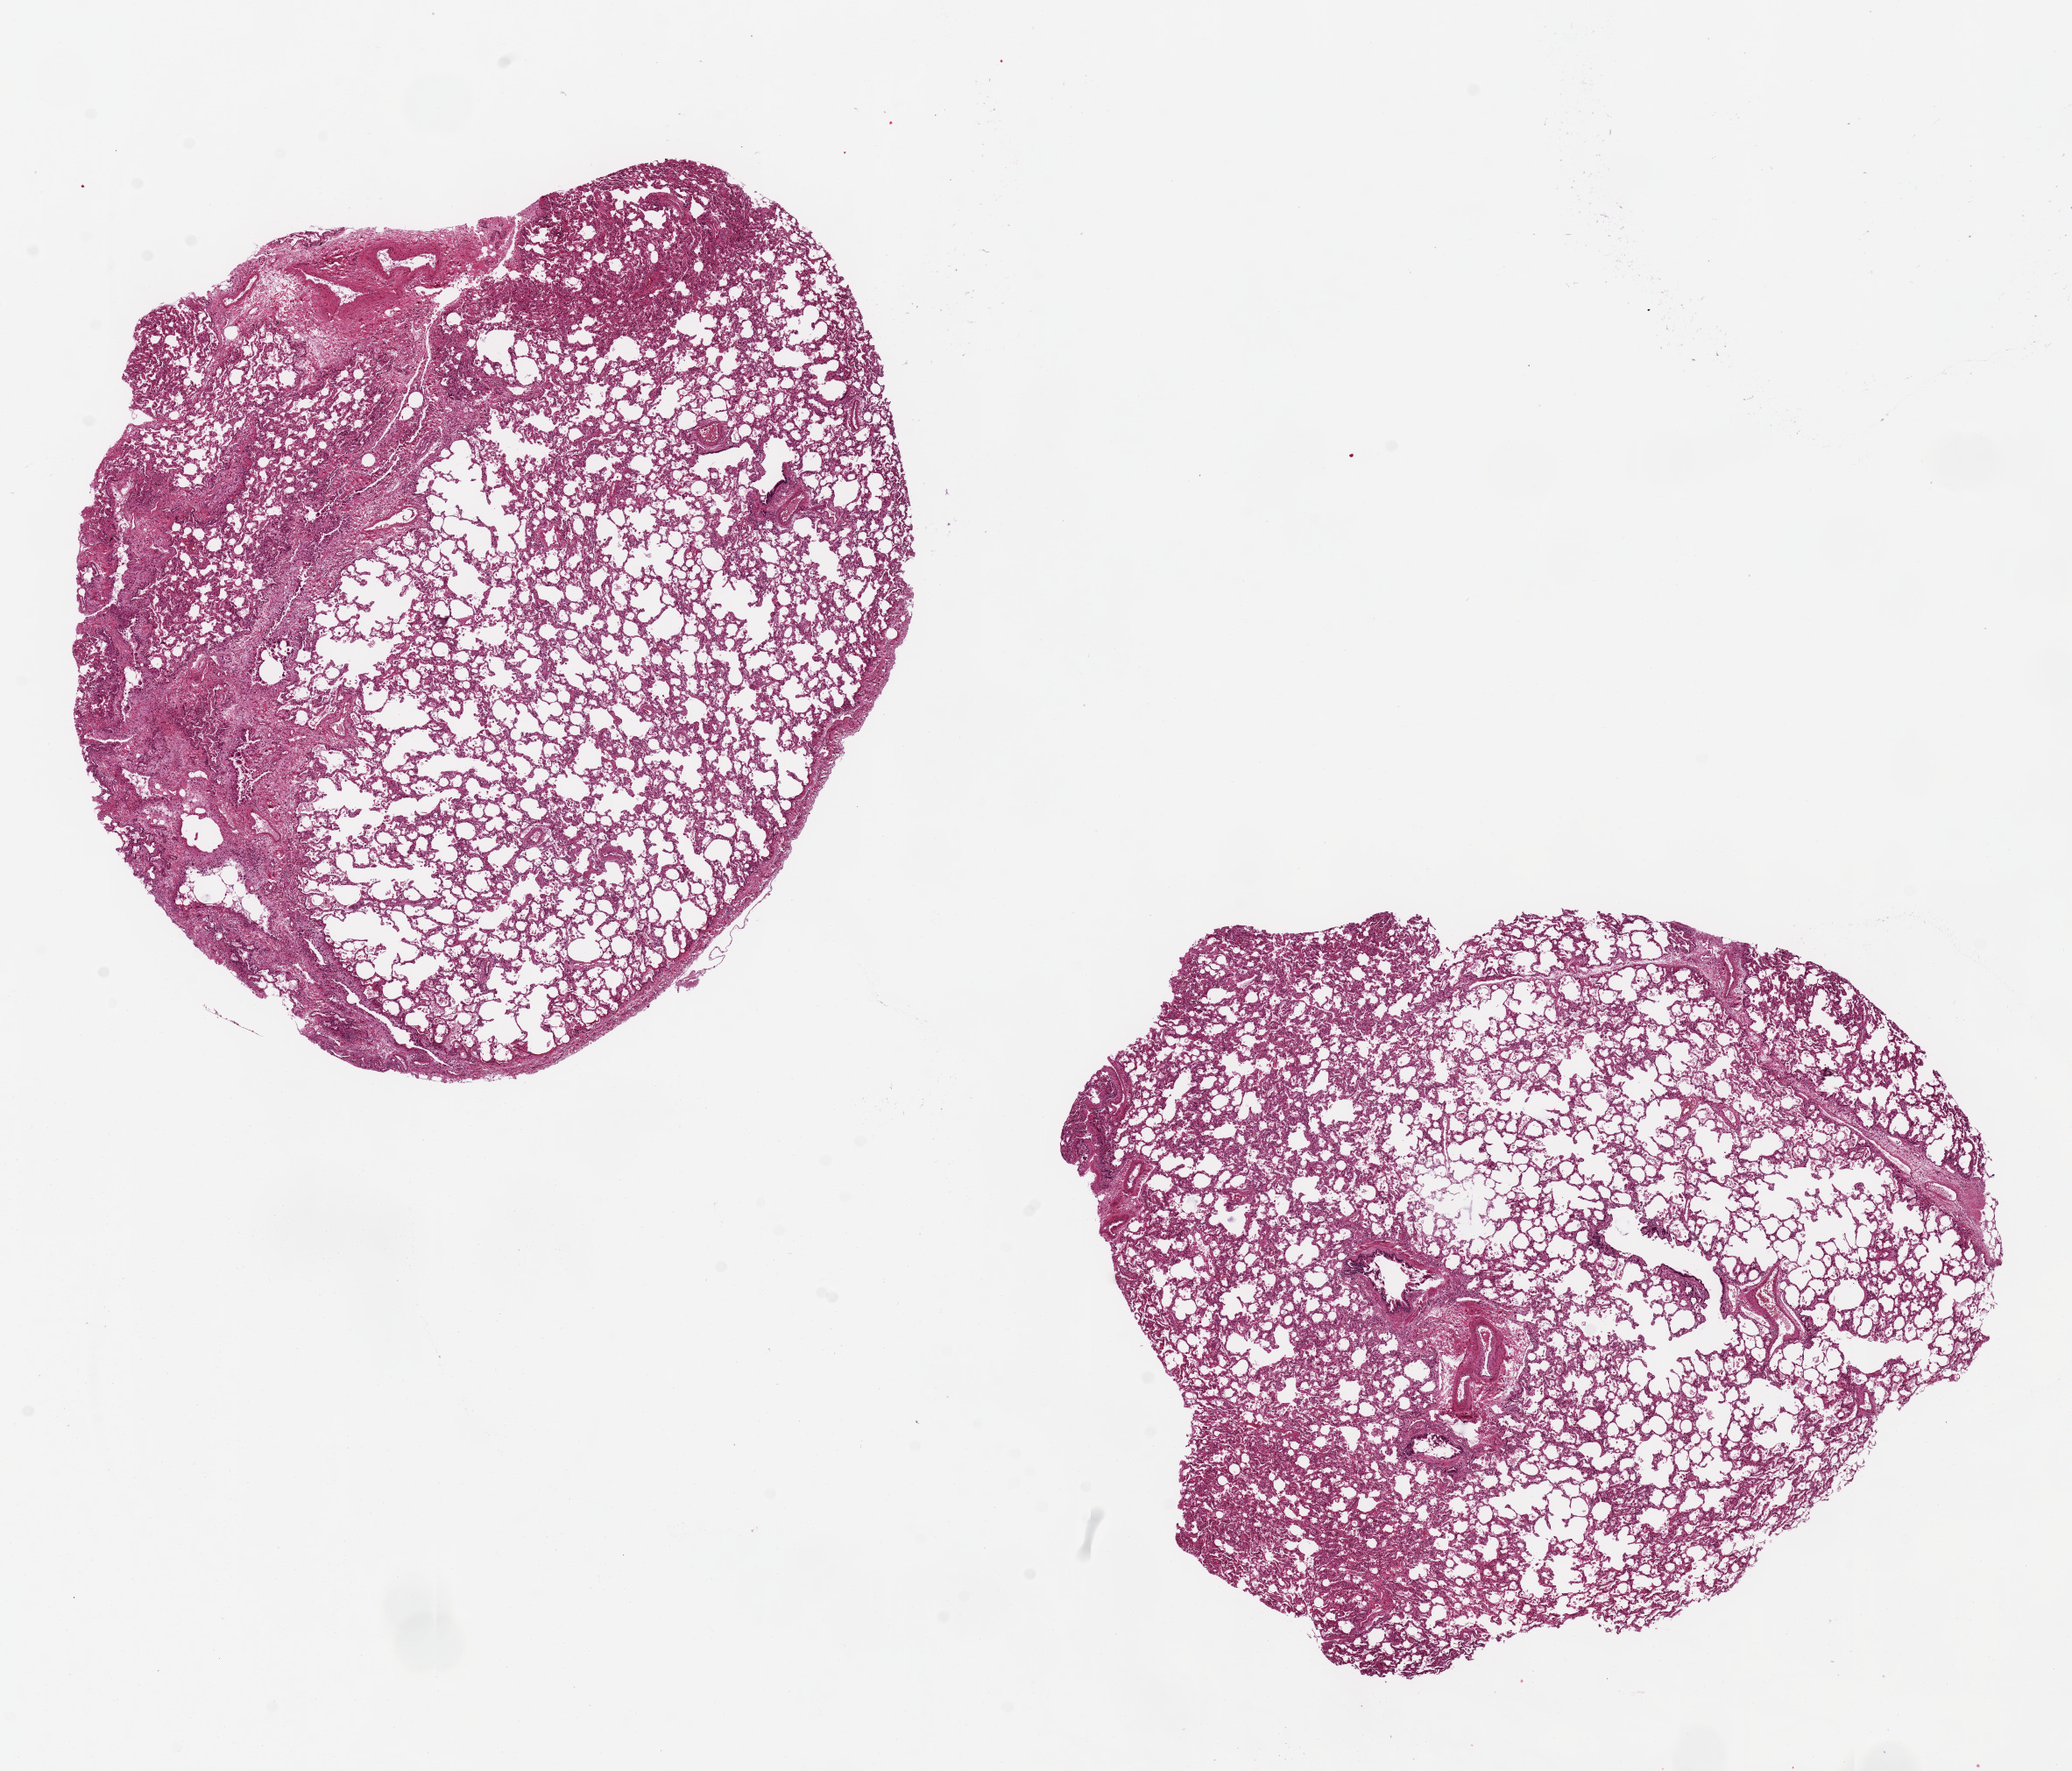
Digitized hematoxylin and eosin (H&E)-stained section — whole scanned area (about 18.7 x 16.0 mm, from a 20x scan) shown as a low-resolution overview; PAXgene-fixed paraffin-embedded (PFPE) section; sampled site (target tissue): lung; donor tissue sample.
Pathologist's review note for this sample: 2 ~ 8.5x7mm aliquots, one with focal fibrosis/consolidation???pending slide review.